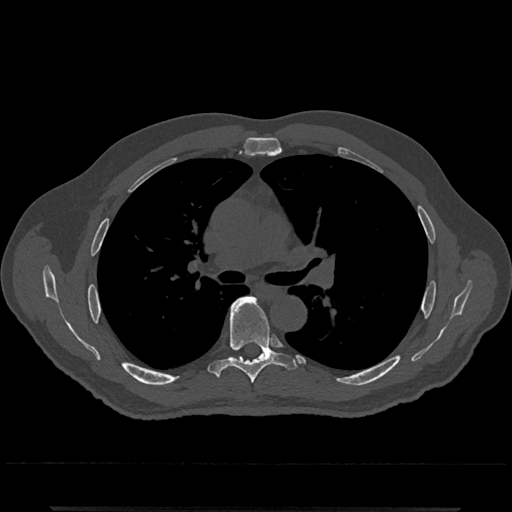
CT including the spine, one axial slice; 120 kVp; bone window (W 1800 / L 400 HU); 0.5 mm slice thickness; 512 × 512 image matrix, field of view 393 × 393 mm. Male patient, age 67 years. Case-level facts recorded for this patient, not image findings: primary cancer: prostate.
Structures marked on this image (semi-automatically segmented with operator editing):
- T6 vertebra: bounding box [x1, y1, x2, y2] px = [208, 296, 296, 384]